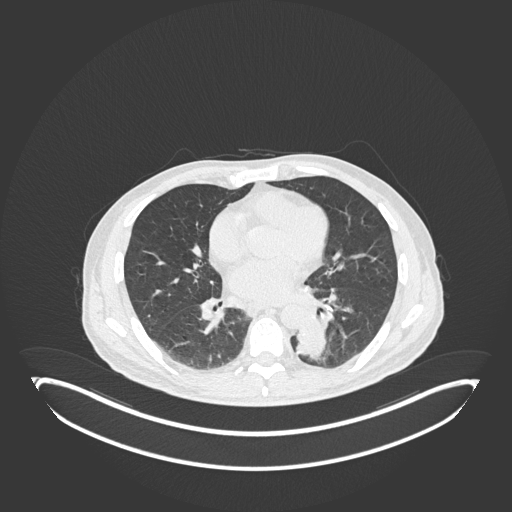
Chest CT, one axial slice; position 81 of 251 along the scan axis; 120 kVp; lung window (W 1500 / L -600 HU); 1 mm slice thickness; 512 × 512 image matrix, field of view 500 × 500 mm. Male patient, age 72 years. From the clinical record (not read from this slice): clinical TNM (as recorded): T2b N0 M1.
Outlined on this slice (bounding box drawn by a radiologist):
- lung tumour (recorded histology: adenocarcinoma): box from (x=297, y=318) to (x=329, y=362) px